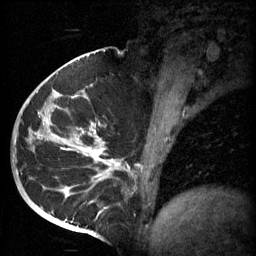
Breast MRI (dynamic contrast-enhanced), one sagittal slice. Position 31 of 60 along the scan axis. 3 images stored at this slice position (order not interpretable as contrast timing). 1.5 T. TE 4.2 ms, TR 11 ms. 2 mm slice thickness. 256 × 256 image matrix, field of view 200 × 200 mm. Female patient, age 51 years.
Structures marked on this image (semi-automatically segmented with operator editing):
- analysis volume of interest (the breast-tissue region the enhancement analysis was run in; not a lesion): bounding box [x1, y1, x2, y2] px = [48, 82, 161, 197]
- tumour enhancement mask (voxels above the 70 % enhancement threshold inside the analysis volume of interest): [52, 90, 143, 197]